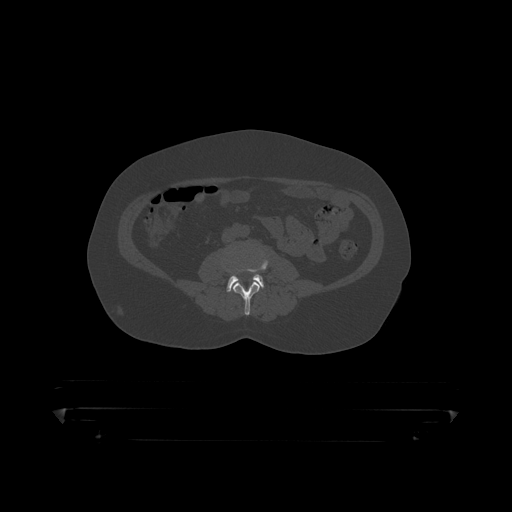
CT including the spine, one axial slice; position 79 of 390 along the scan axis; reconstruction kernel STANDARD; 120 kVp; bone window (W 1800 / L 400 HU); 512 × 512 image matrix. Patient: male, 60 years. From the clinical record (not read from this slice): primary cancer: prostate.
Structures marked on this image (semi-automatically segmented with operator editing):
- L3 vertebra: bounding box (x1, y1, x2, y2) in pixels: (232, 253, 269, 316)
- L4 vertebra: (227, 269, 264, 292)